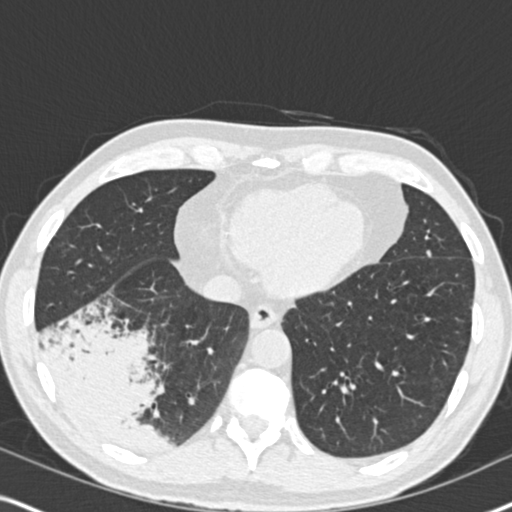
Low-dose screening chest CT, one axial slice; slice 63 of 182 in the series (ordered by position); reconstruction kernel B30f; 120 kVp; lung window (W 1500 / L -600 HU); 2 mm slice thickness; 512 × 512 image matrix, field of view 330 × 330 mm.
Annotated regions visible in this slice (manually delineated by an expert):
- lesion 1 (tumor, lower lobe of right lung): bounding box [x1, y1, x2, y2] px = [47, 324, 163, 451]